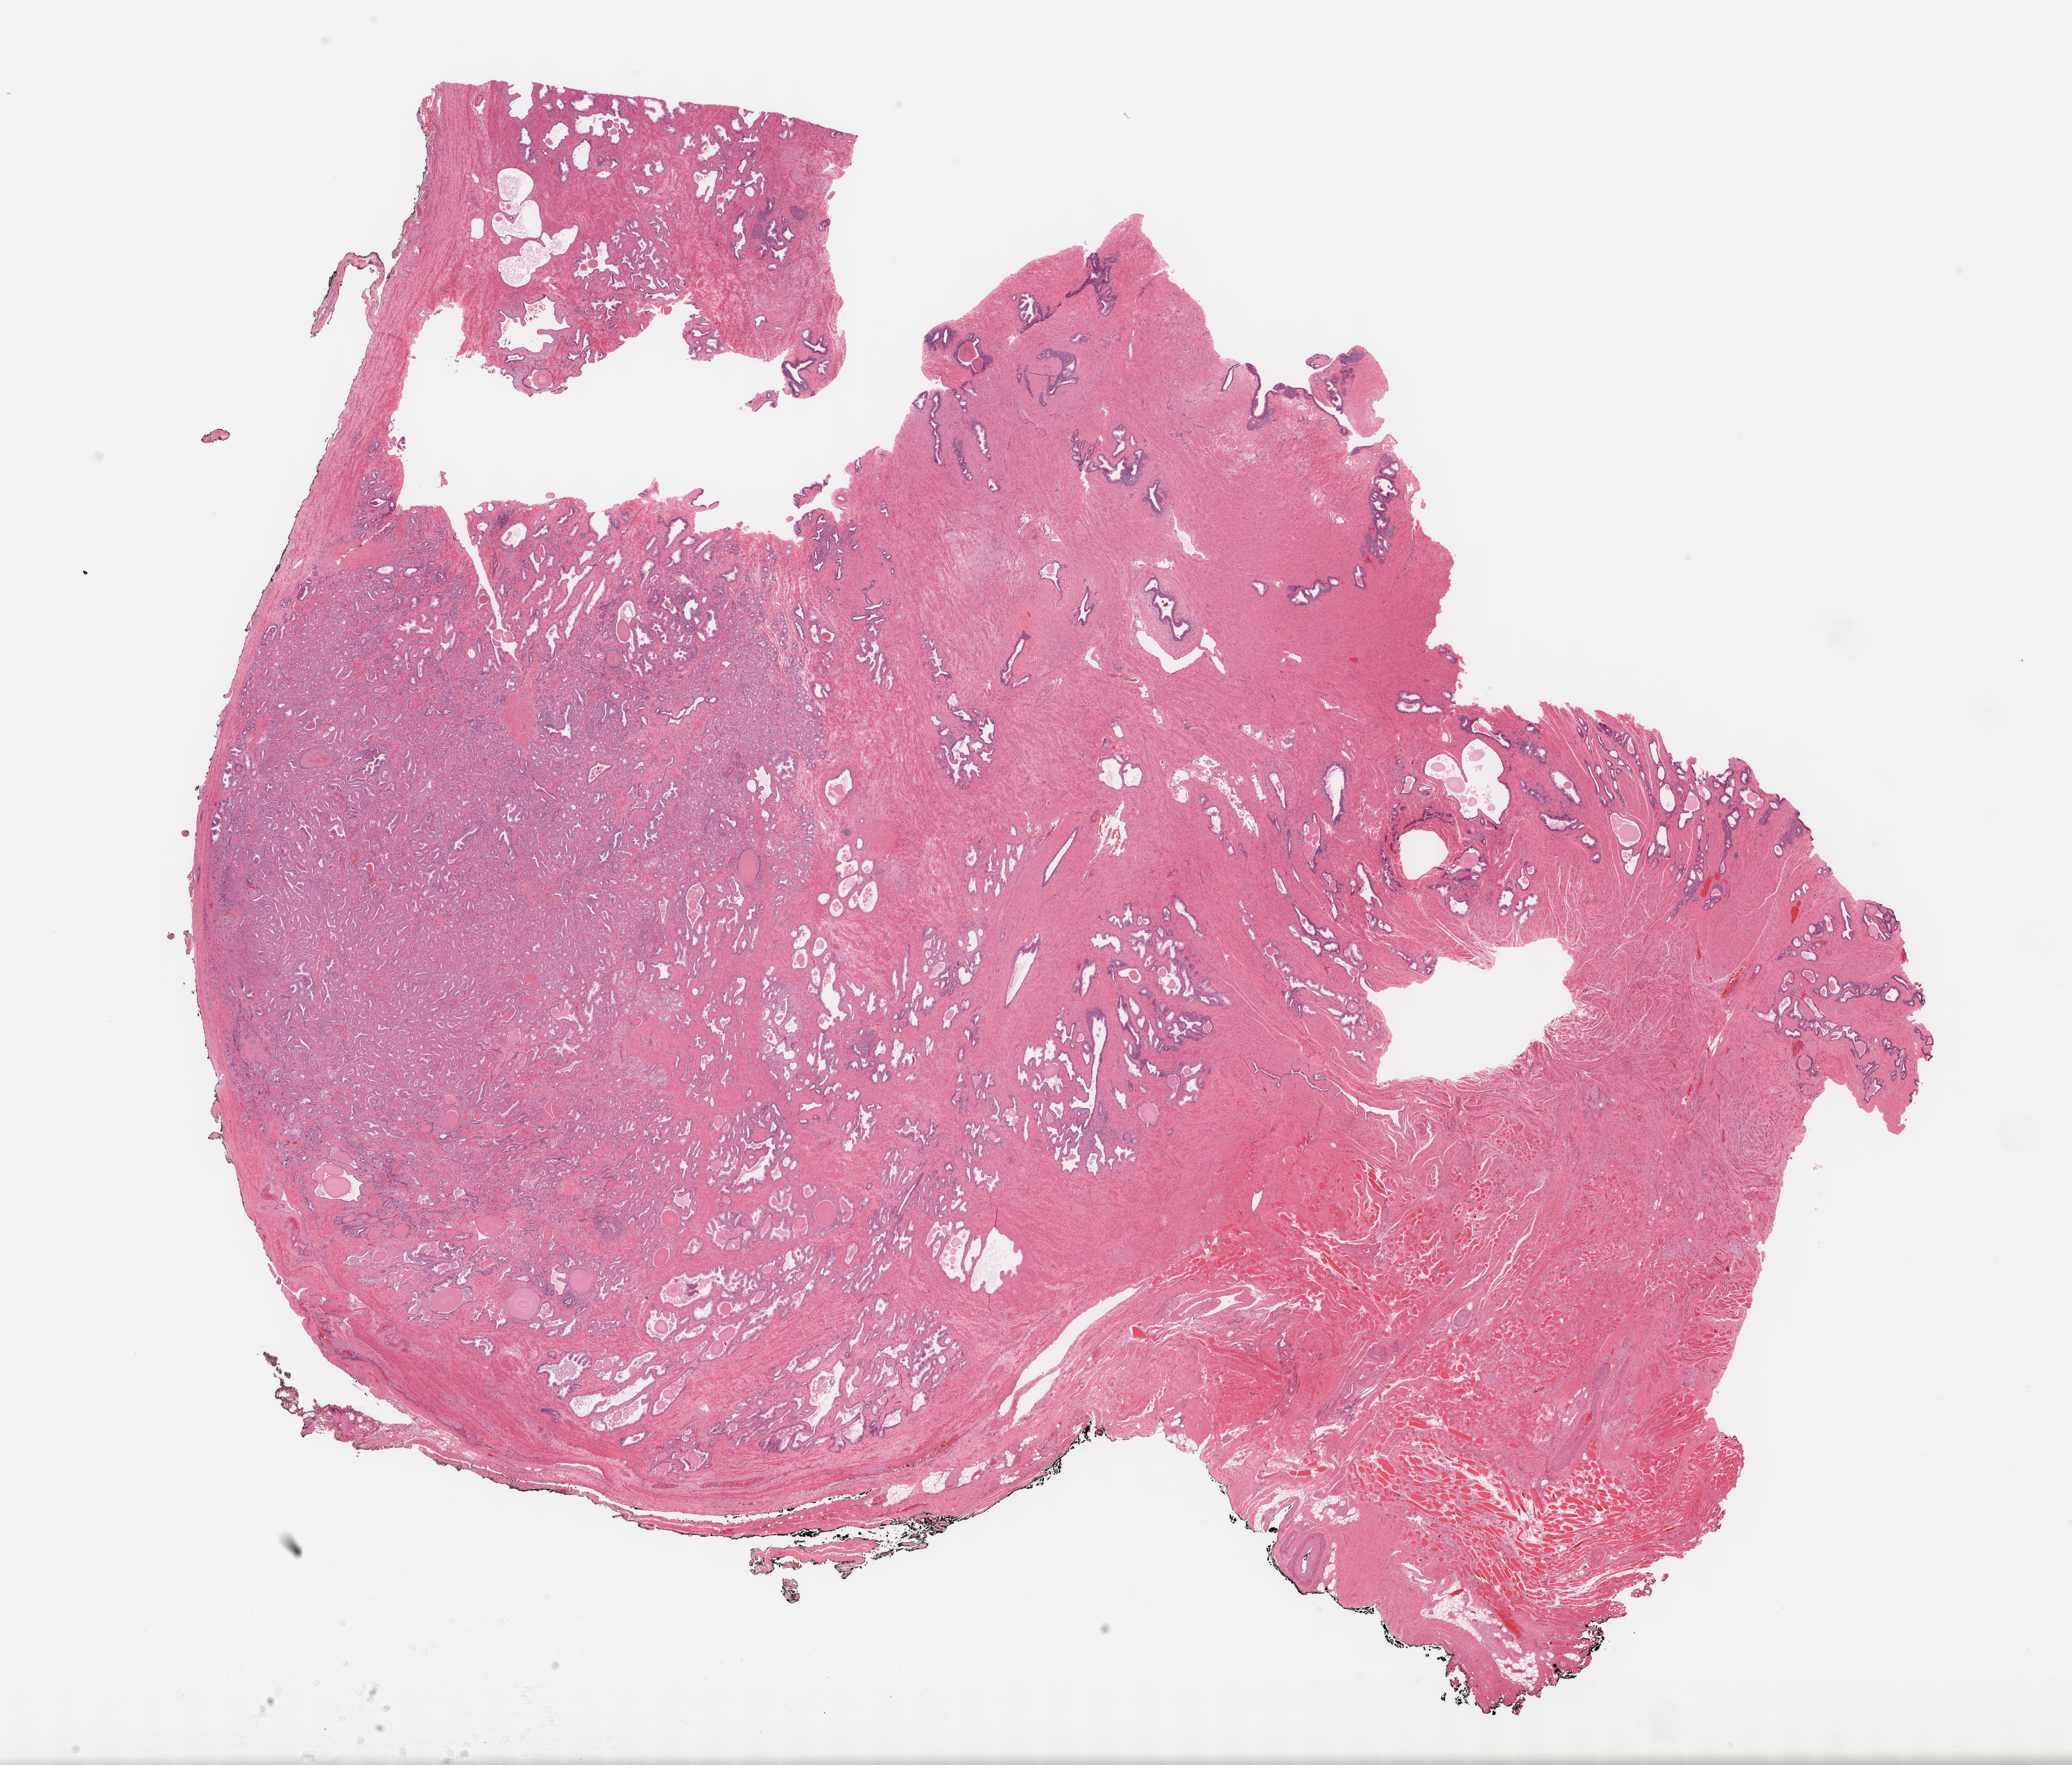
Digitized Hematoxylin and eosin (H&E) stained tissue section (whole slide), low-resolution overview of the scanned area, about 24.2 x 20.6 mm (slide scanned at 40x); FFPE section; sample: primary tumour, prostate. Male, age 61 years at initial diagnosis. Gleason score: 7 (3+4).
- pathologic diagnosis: Adenocarcinoma, NOS (prostate gland)